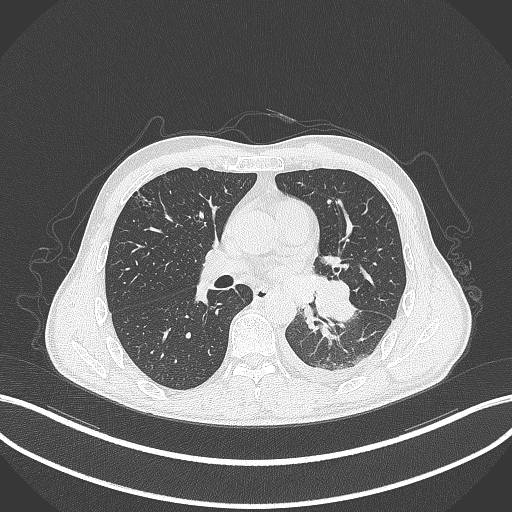
Chest CT, one axial slice. Position 169 of 295 along the scan axis. 120 kVp. Lung window (W 1500 / L -600 HU). 1 mm slice thickness. 512 × 512 image matrix, field of view 400 × 400 mm. Patient: male, 47 years. From the clinical record (not read from this slice): clinical TNM (as recorded): T3 N1 M1c.
Annotated regions visible in this slice (rectangle marked by the reading radiologist):
- lung tumour (recorded histology: small cell carcinoma): bounding box (x1, y1, x2, y2) in pixels: (315, 276, 356, 325)